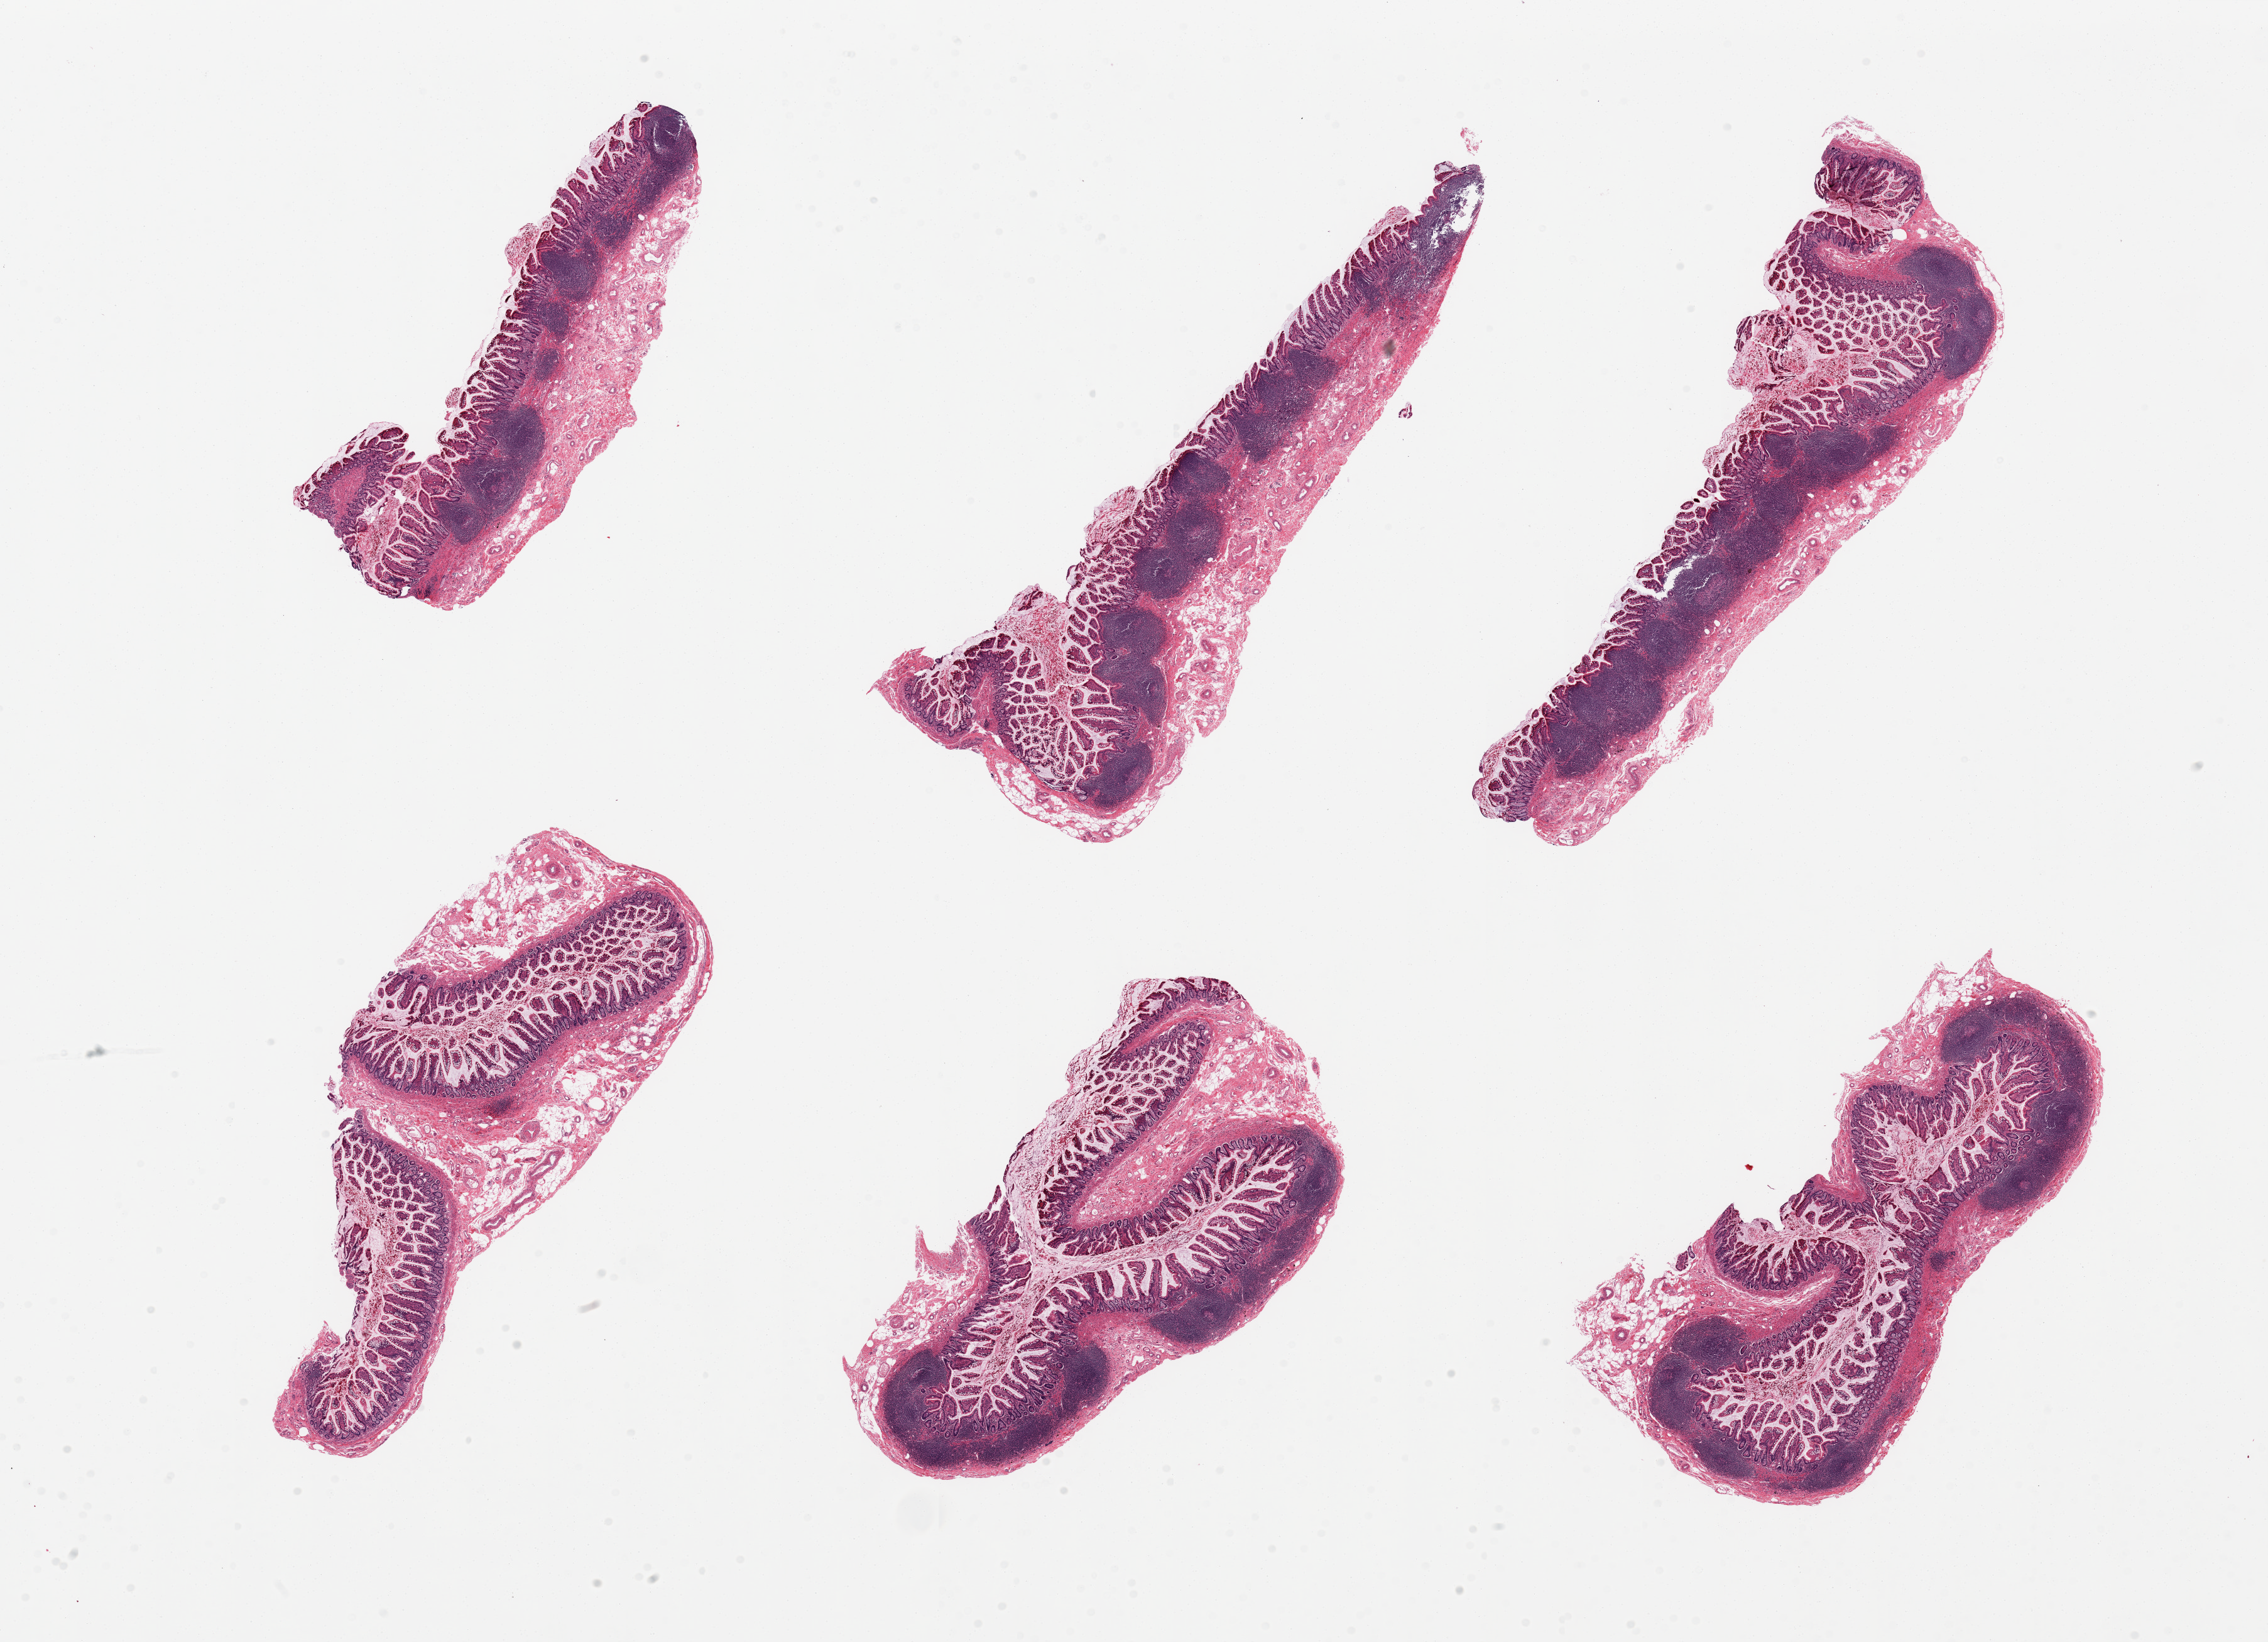
Digitized H&E-stained section — whole scanned area (about 28.5 x 20.7 mm) shown as a low-resolution overview. PAXgene-fixed, paraffin-embedded tissue. Sampled site (target tissue): ileum. Tissue donor sample.
Review note (as recorded): 6 pieces, good specimen, well preserved, well trimmed, good representation of lymphoid tissue.